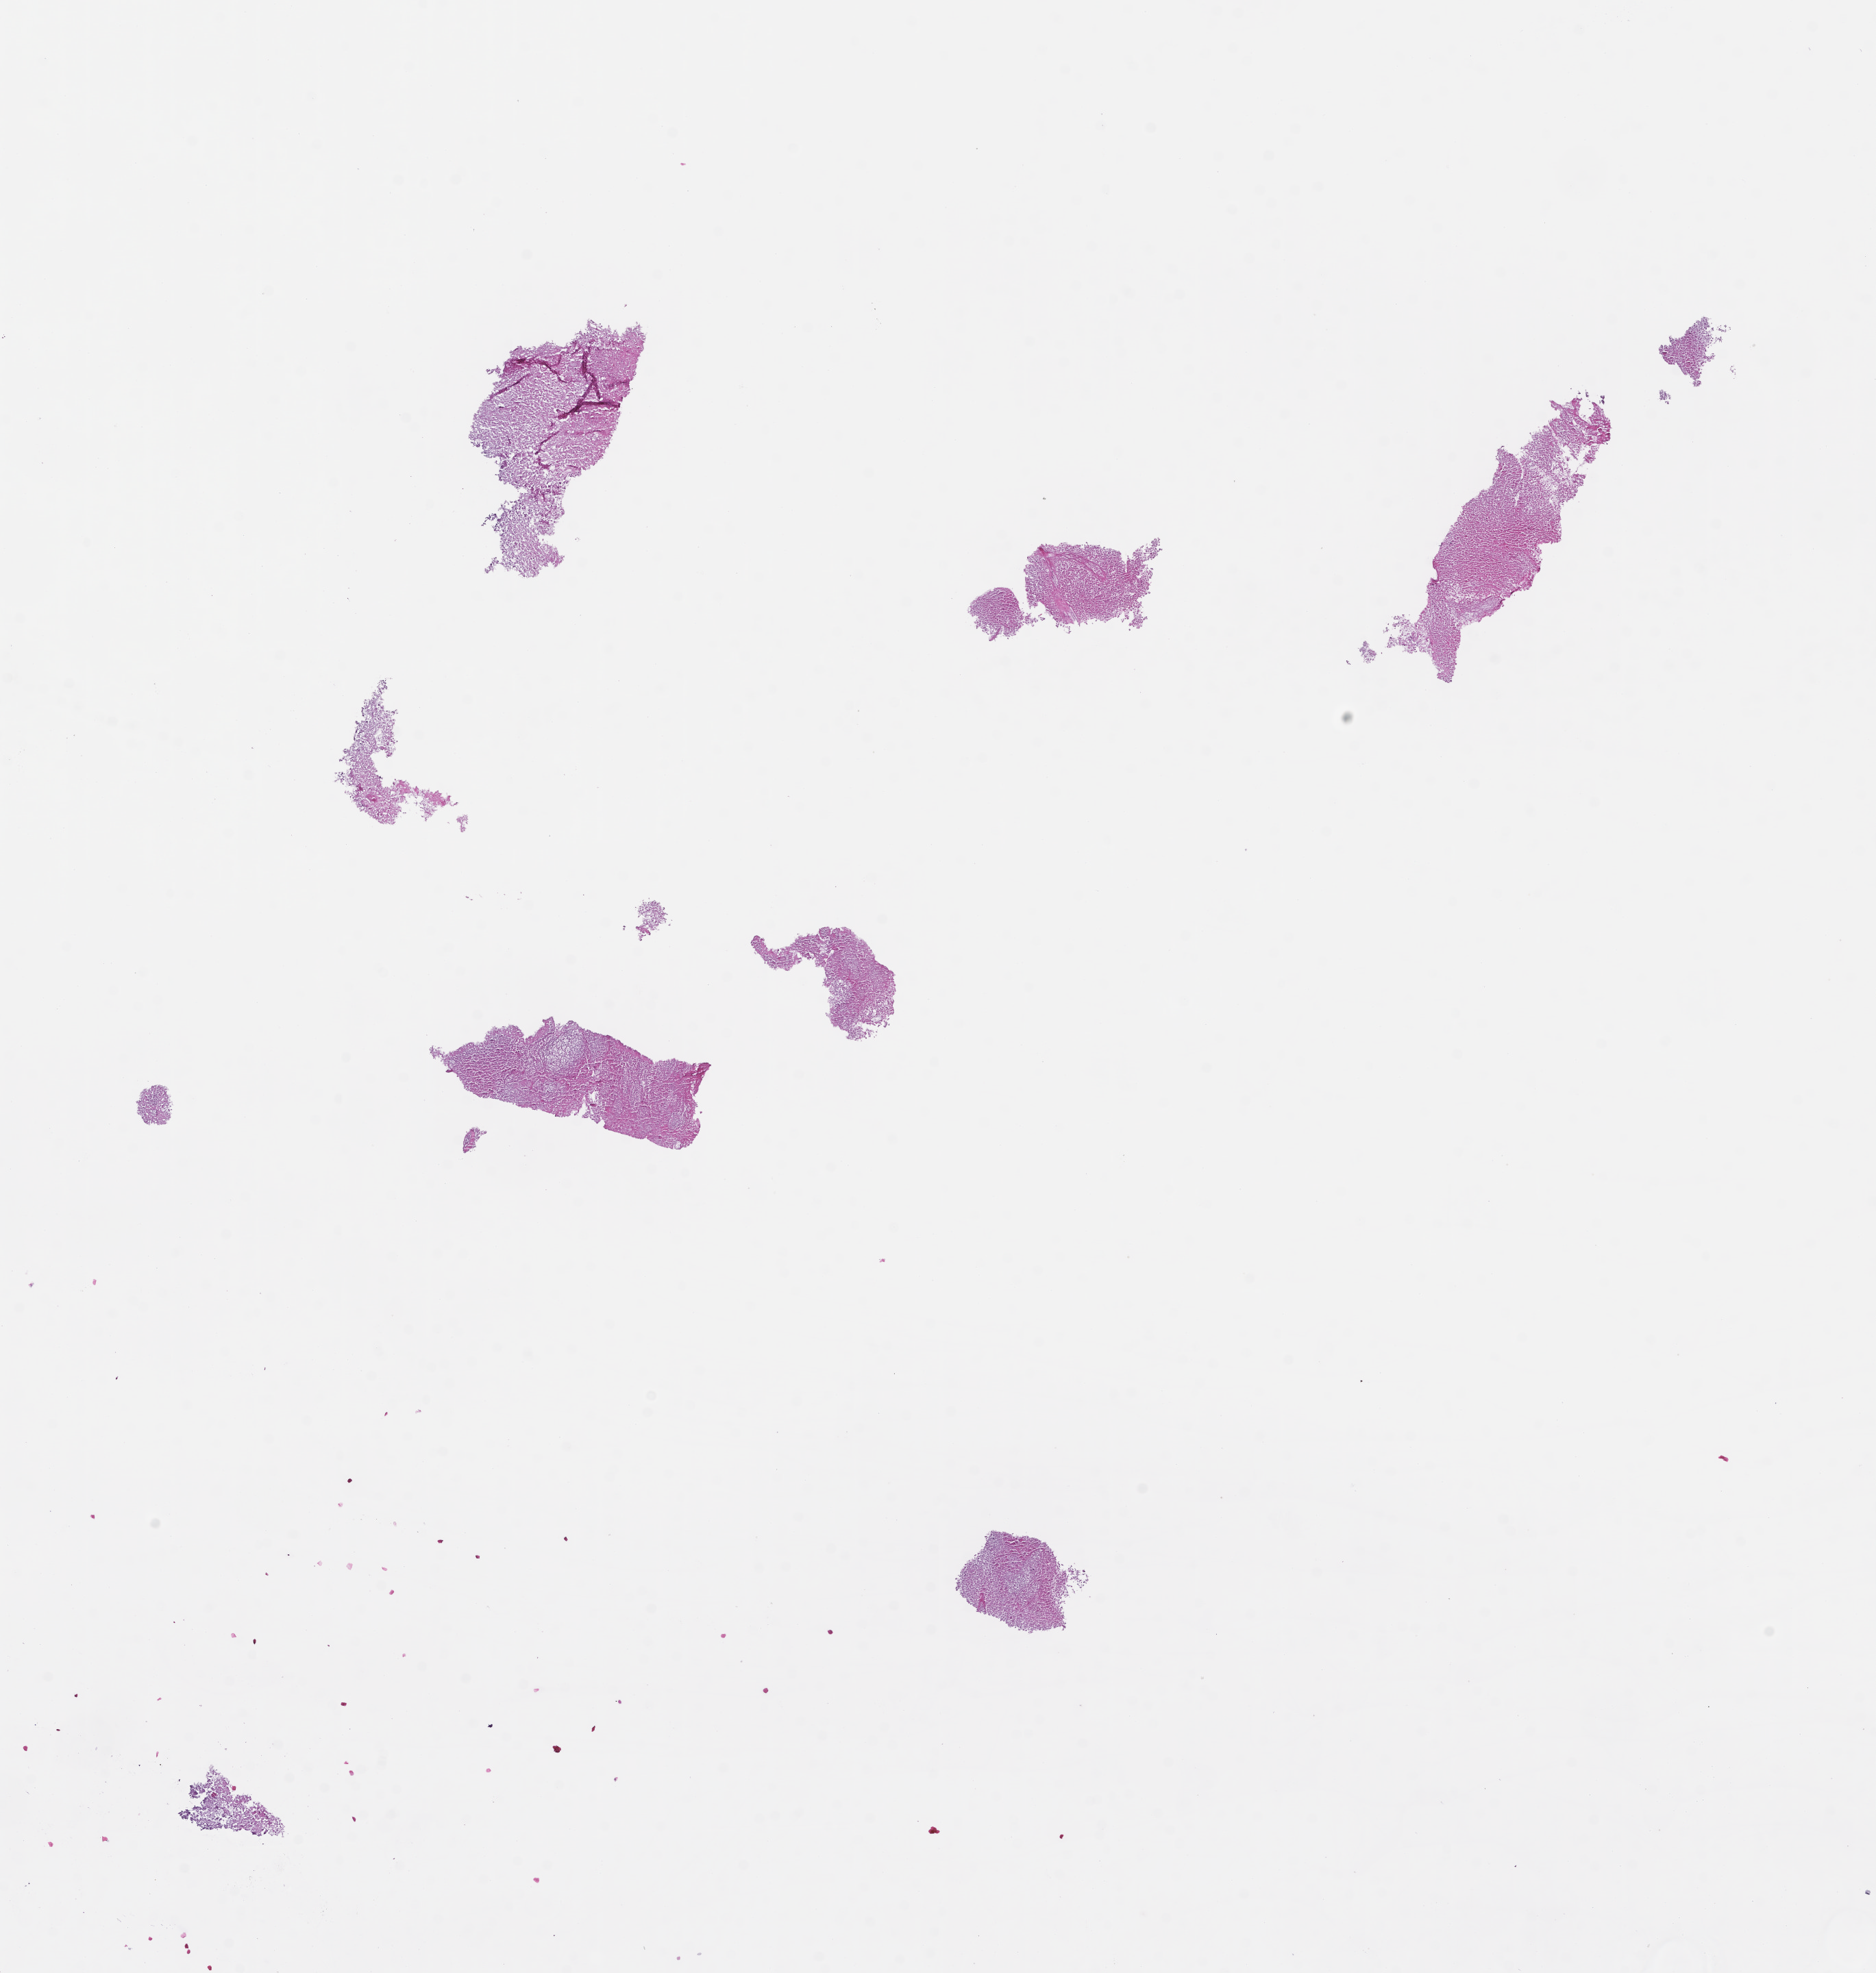
Digitized H&E-stained section — shown as a low-resolution overview of the whole scanned area (about 11.1 x 11.6 mm), formalin-fixed, paraffin-embedded (FFPE) tissue, specimen time point: collected at baseline (before treatment). Patient: female.
This section: metastasis (sampled organ not recorded). Primary diagnosis of the patient: Colorectal Carcinoma.